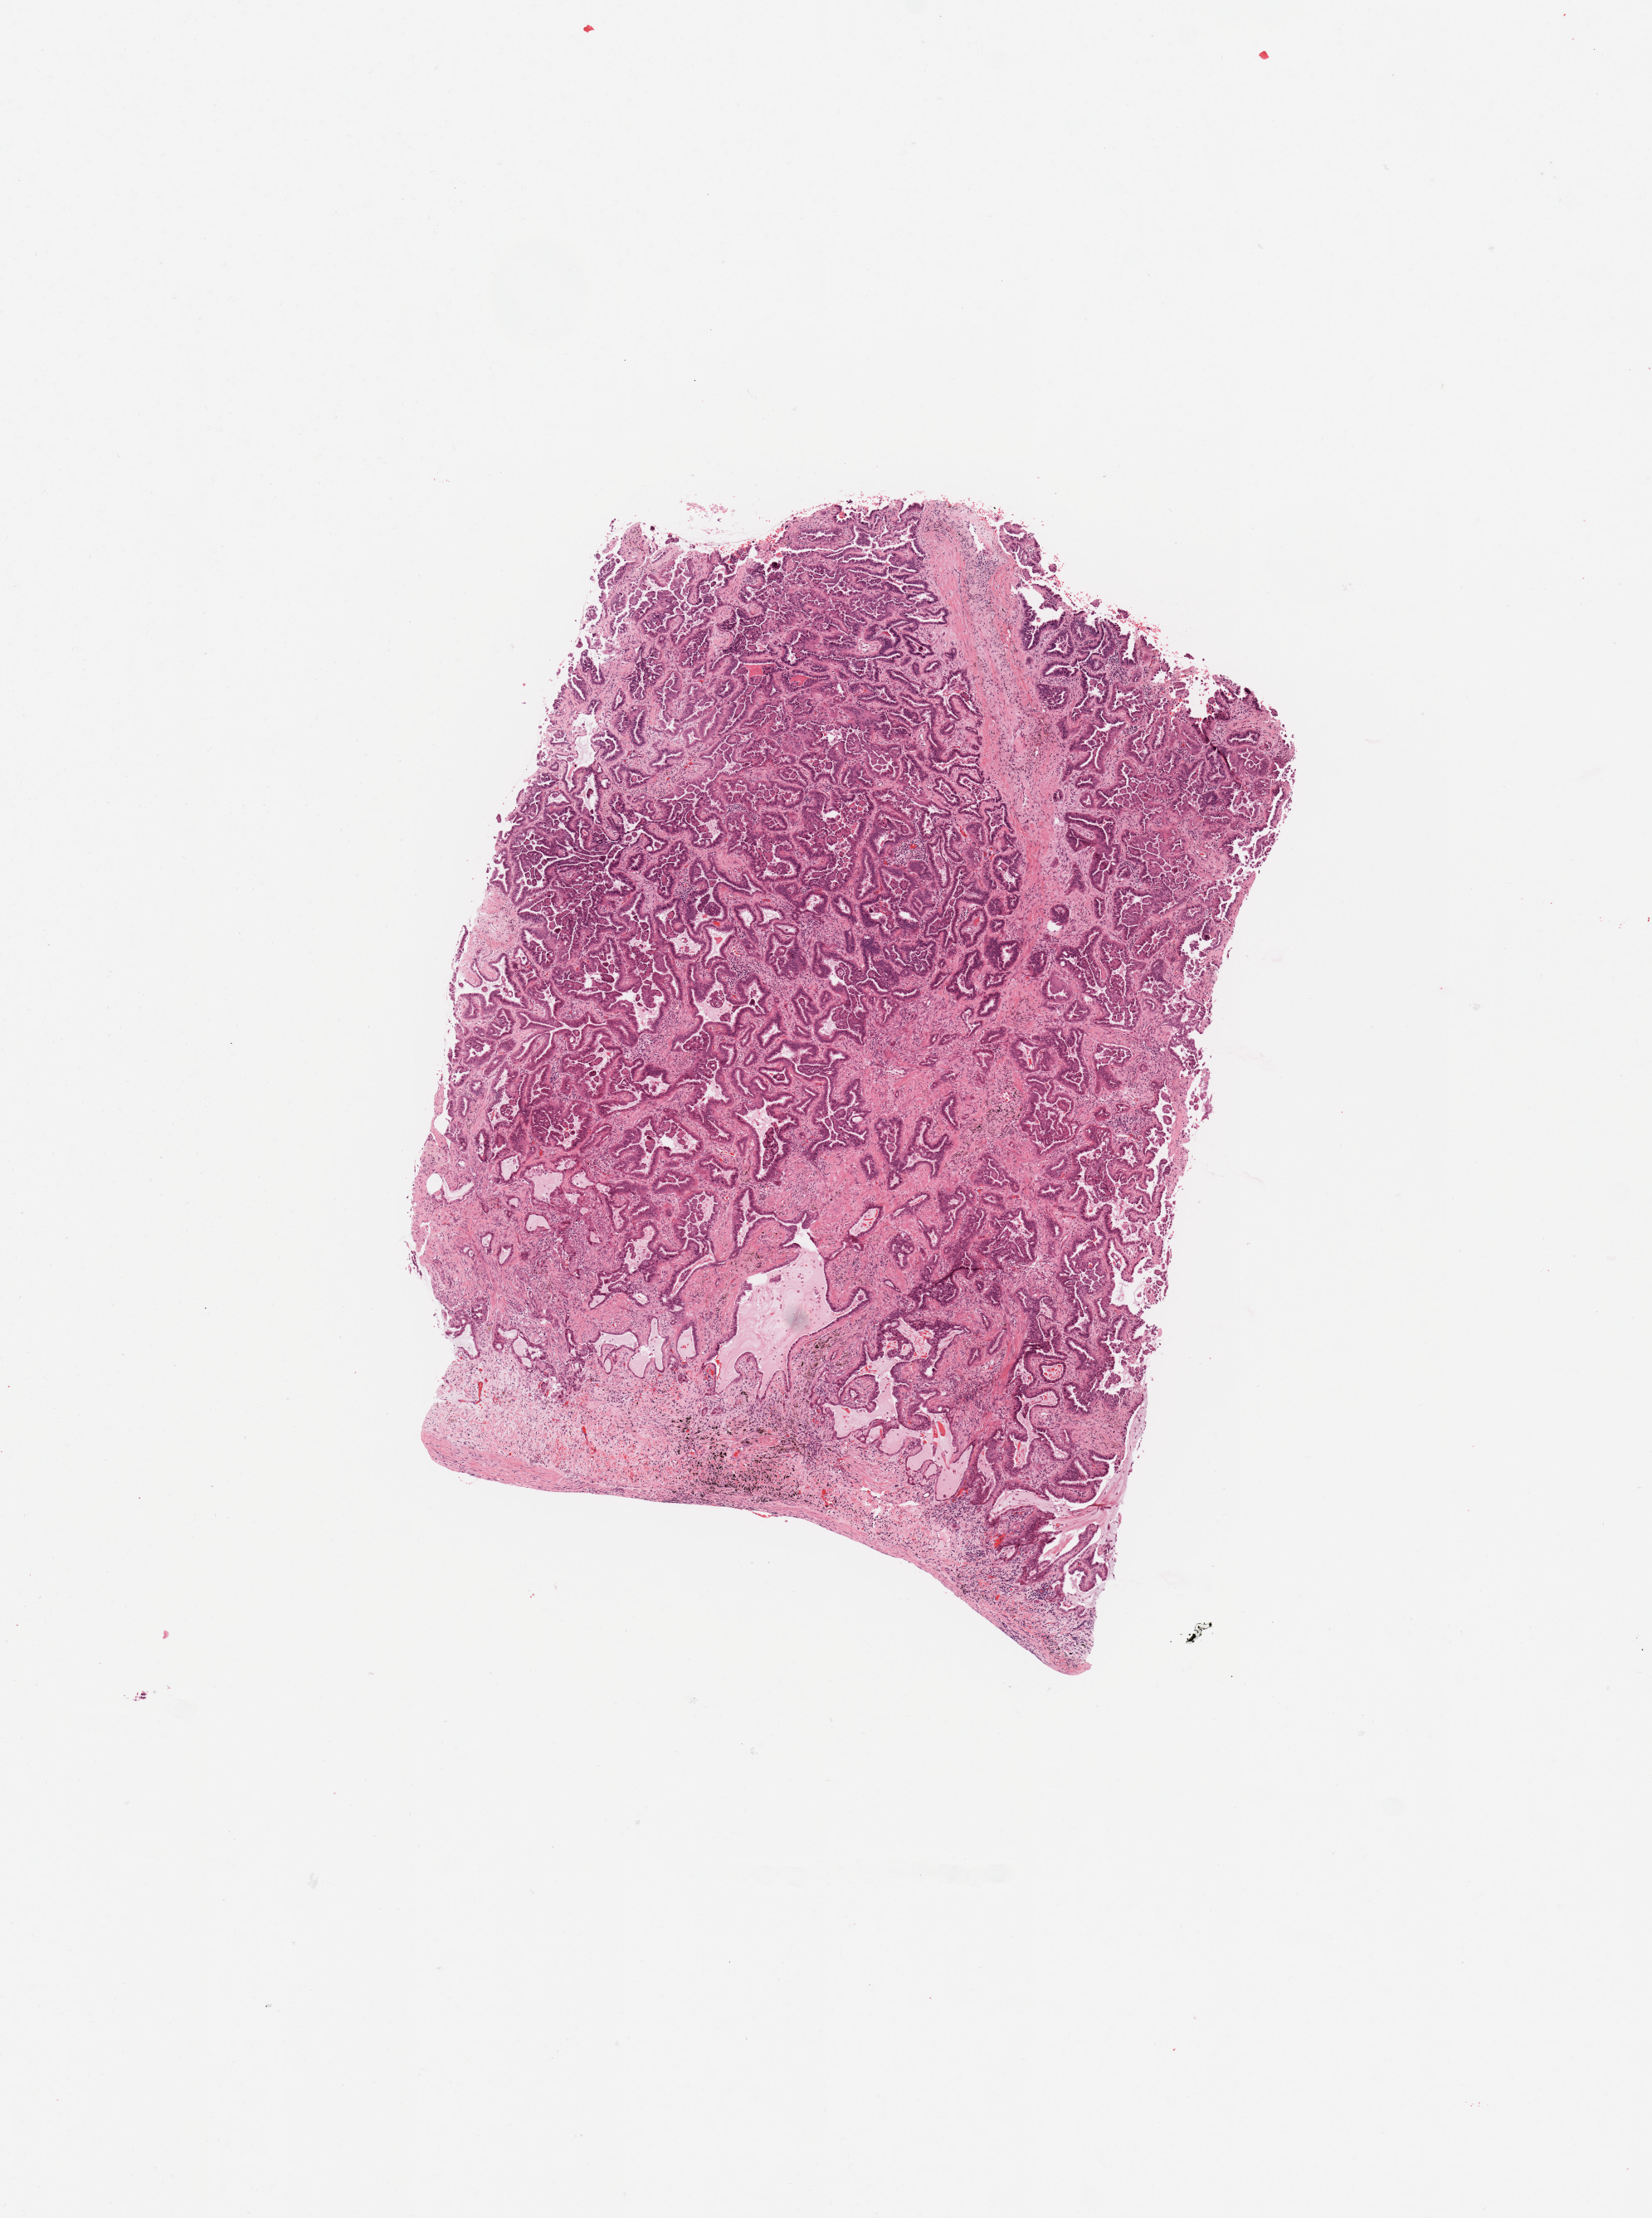
Whole-slide histology image, Hematoxylin and eosin (H&E) stained, whole scanned area (about 7.9 x 10.6 mm, acquisition: 20x scan) shown as a low-resolution overview; tumour tissue sample, sampled site: lung. 73-year-old male patient. Pathologist review of this section (percent, as recorded): tumour nuclei 75%, necrosis 0%.
Histologic diagnosis: Adenocarcinoma, NOS.